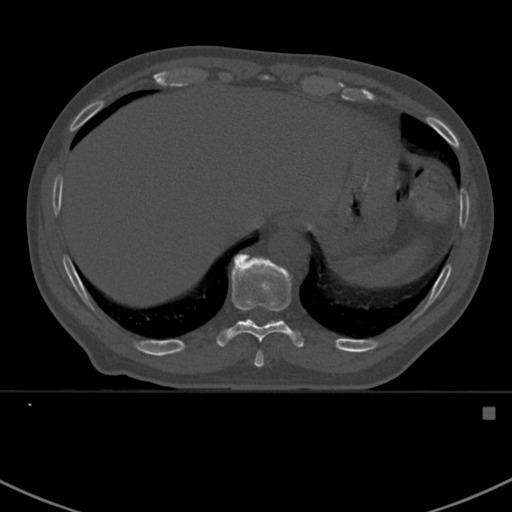
CT including the spine, one axial slice. Position 365 of 412 along the scan axis. Reconstruction kernel Br40s. Bone window (W 1800 / L 400 HU). 512 × 512 image matrix. Patient: male, 59 years. Case-level facts recorded for this patient, not image findings: primary cancer: prostate.
Outlined on this slice (semi-automatically segmented with operator editing):
- T10 vertebra: box from (x=217, y=254) to (x=304, y=367) px
- T9 vertebra: (x=255, y=351)–(x=263, y=363)